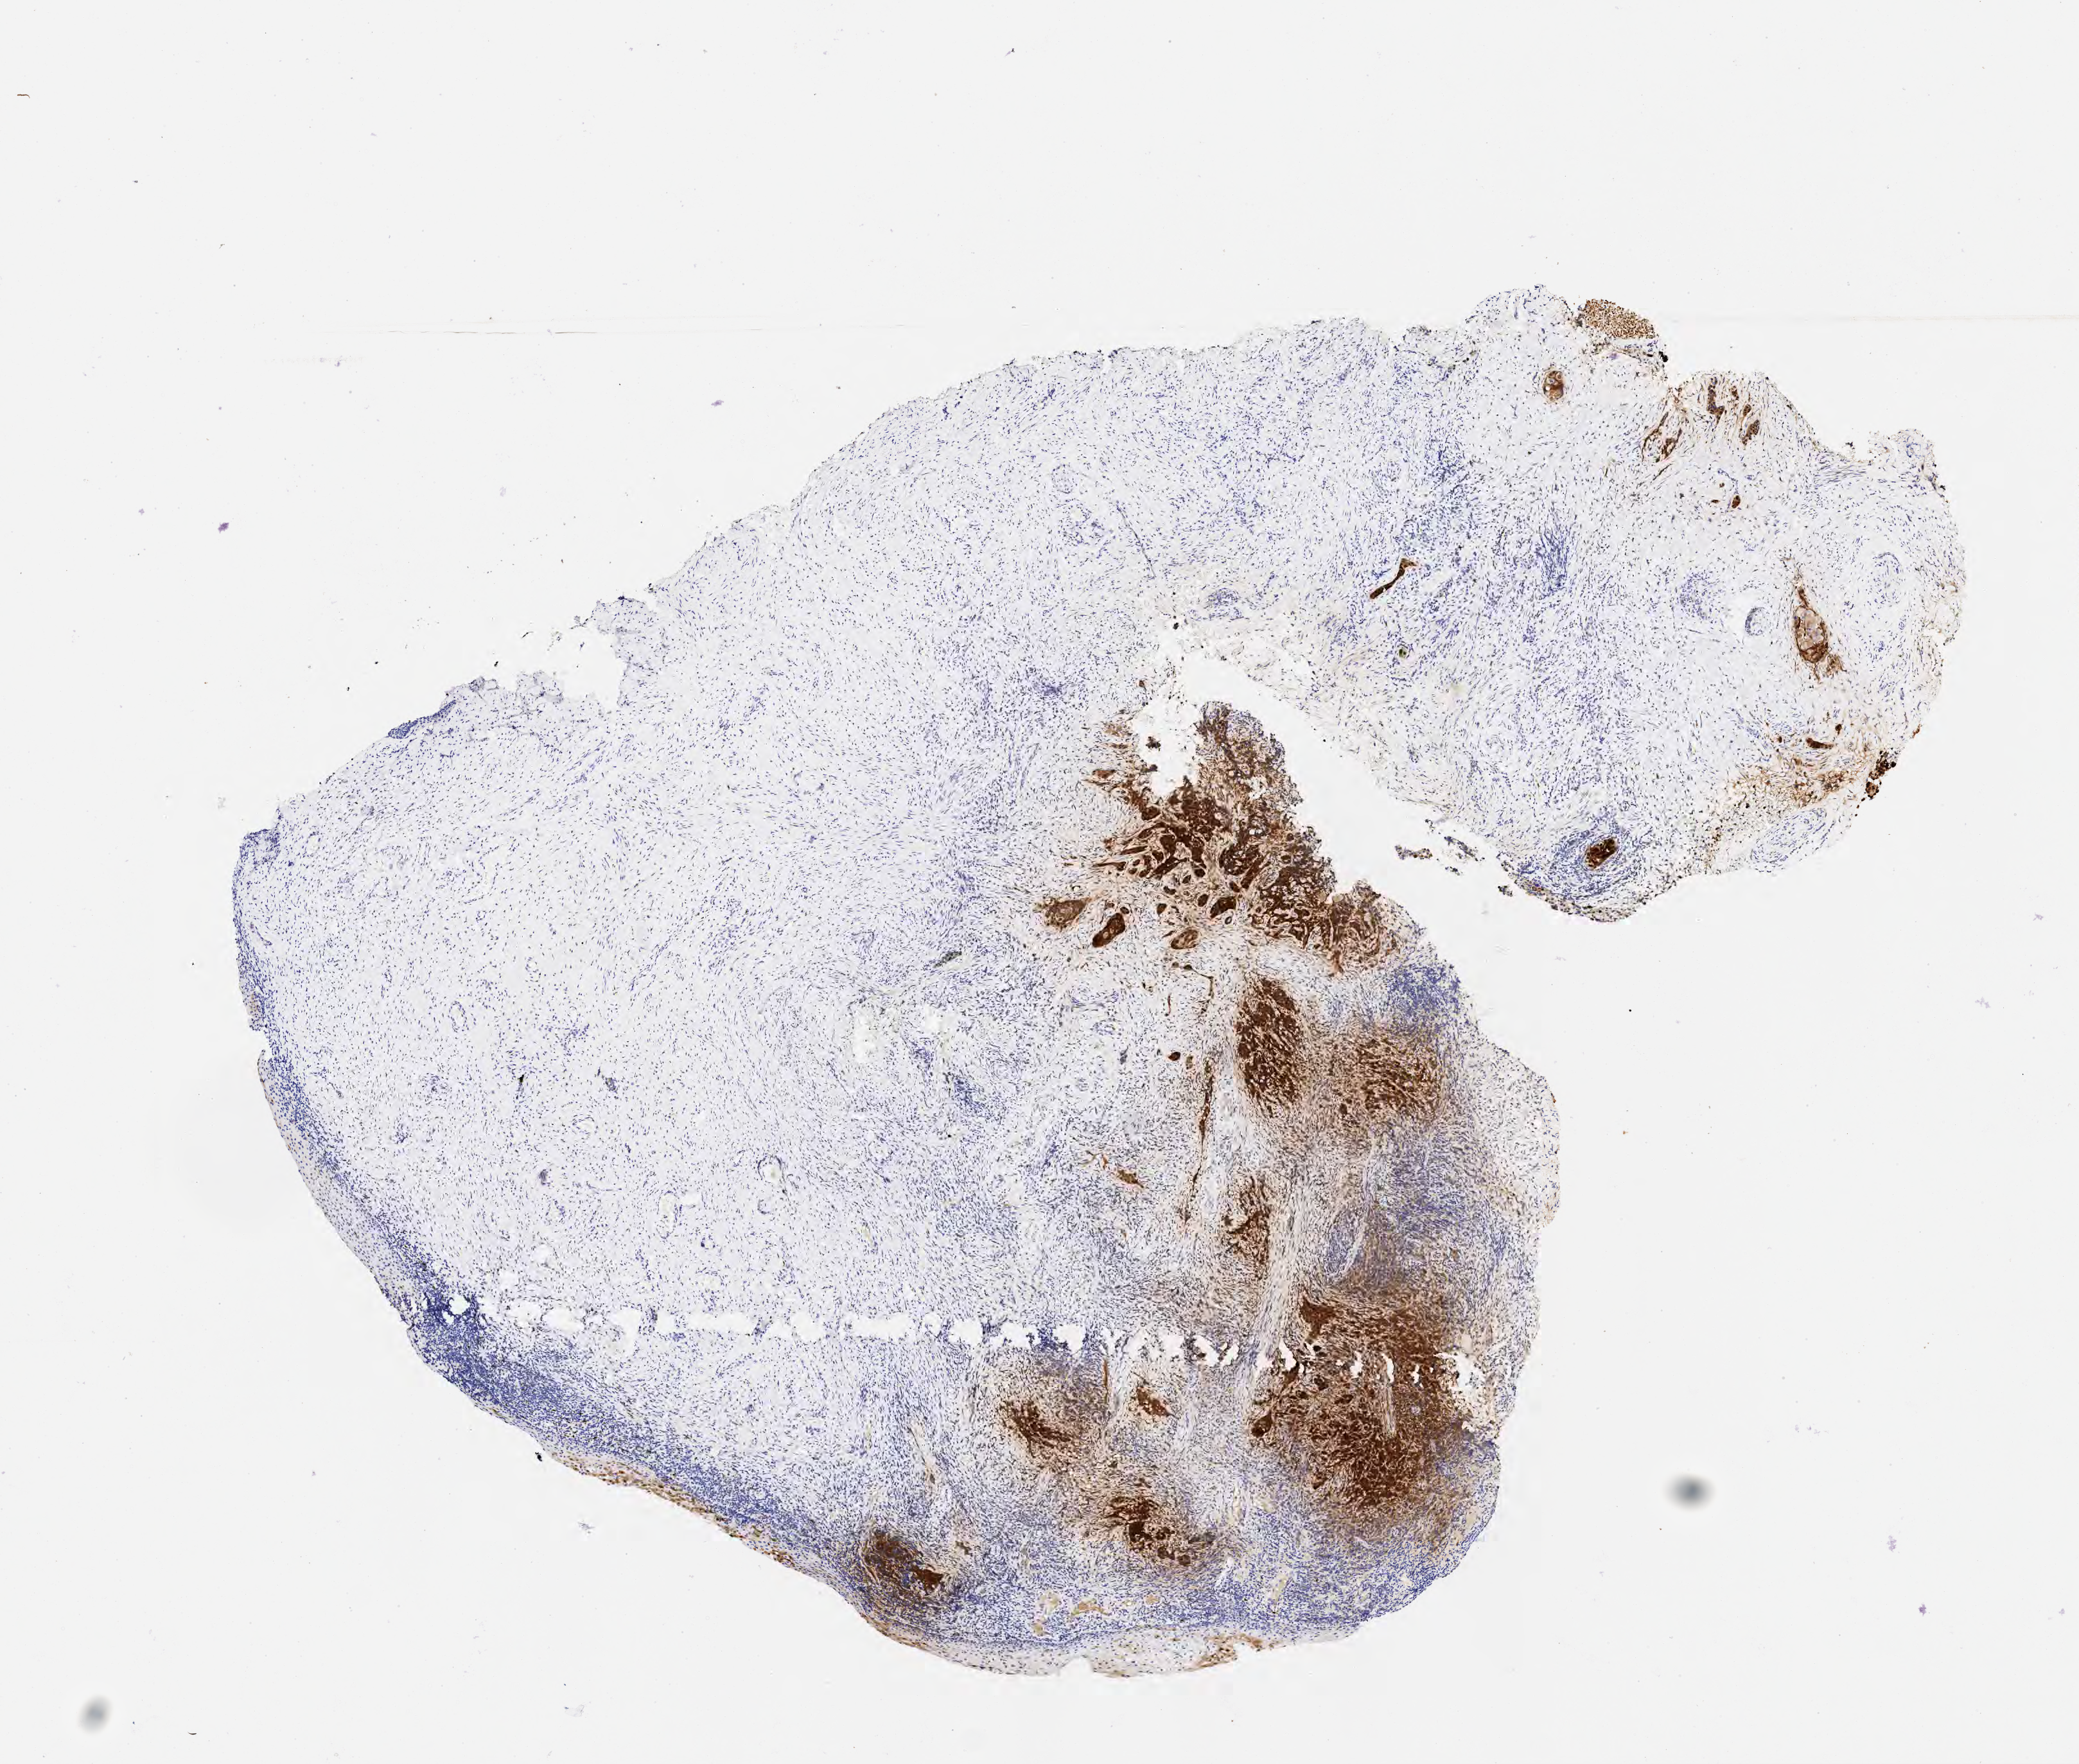
Whole-slide image, immunohistochemical stain for p16 (p16INK4a) — a low-resolution overview of the entire scanned area, about 6.5 x 5.5 mm. Specimen: tumor tissue. Site: cervix. Female patient, 68 years old.
Histologic diagnosis: Squamous cell carcinoma, large cell, nonkeratinizing, NOS.